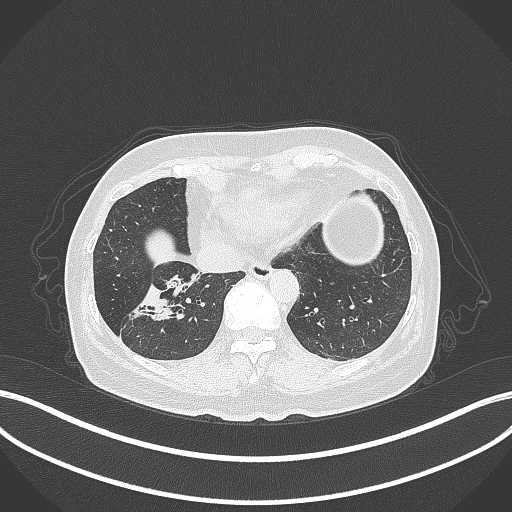
Chest CT, one axial slice. Position 109 of 429 along the scan axis. Reconstruction kernel B70f. Lung window (W 1500 / L -600 HU). 1 mm slice thickness. 512 × 512 image matrix, field of view 400 × 400 mm. Female patient, age 67 years. Case-level facts recorded for this patient, not image findings: clinical TNM (as recorded): T1c N1 M0; histopathological grade: G2-3.
Outlined on this slice (rectangle marked by the reading radiologist):
- lung tumour (recorded histology: adenocarcinoma): bounding box [x1, y1, x2, y2] px = [126, 274, 193, 327]